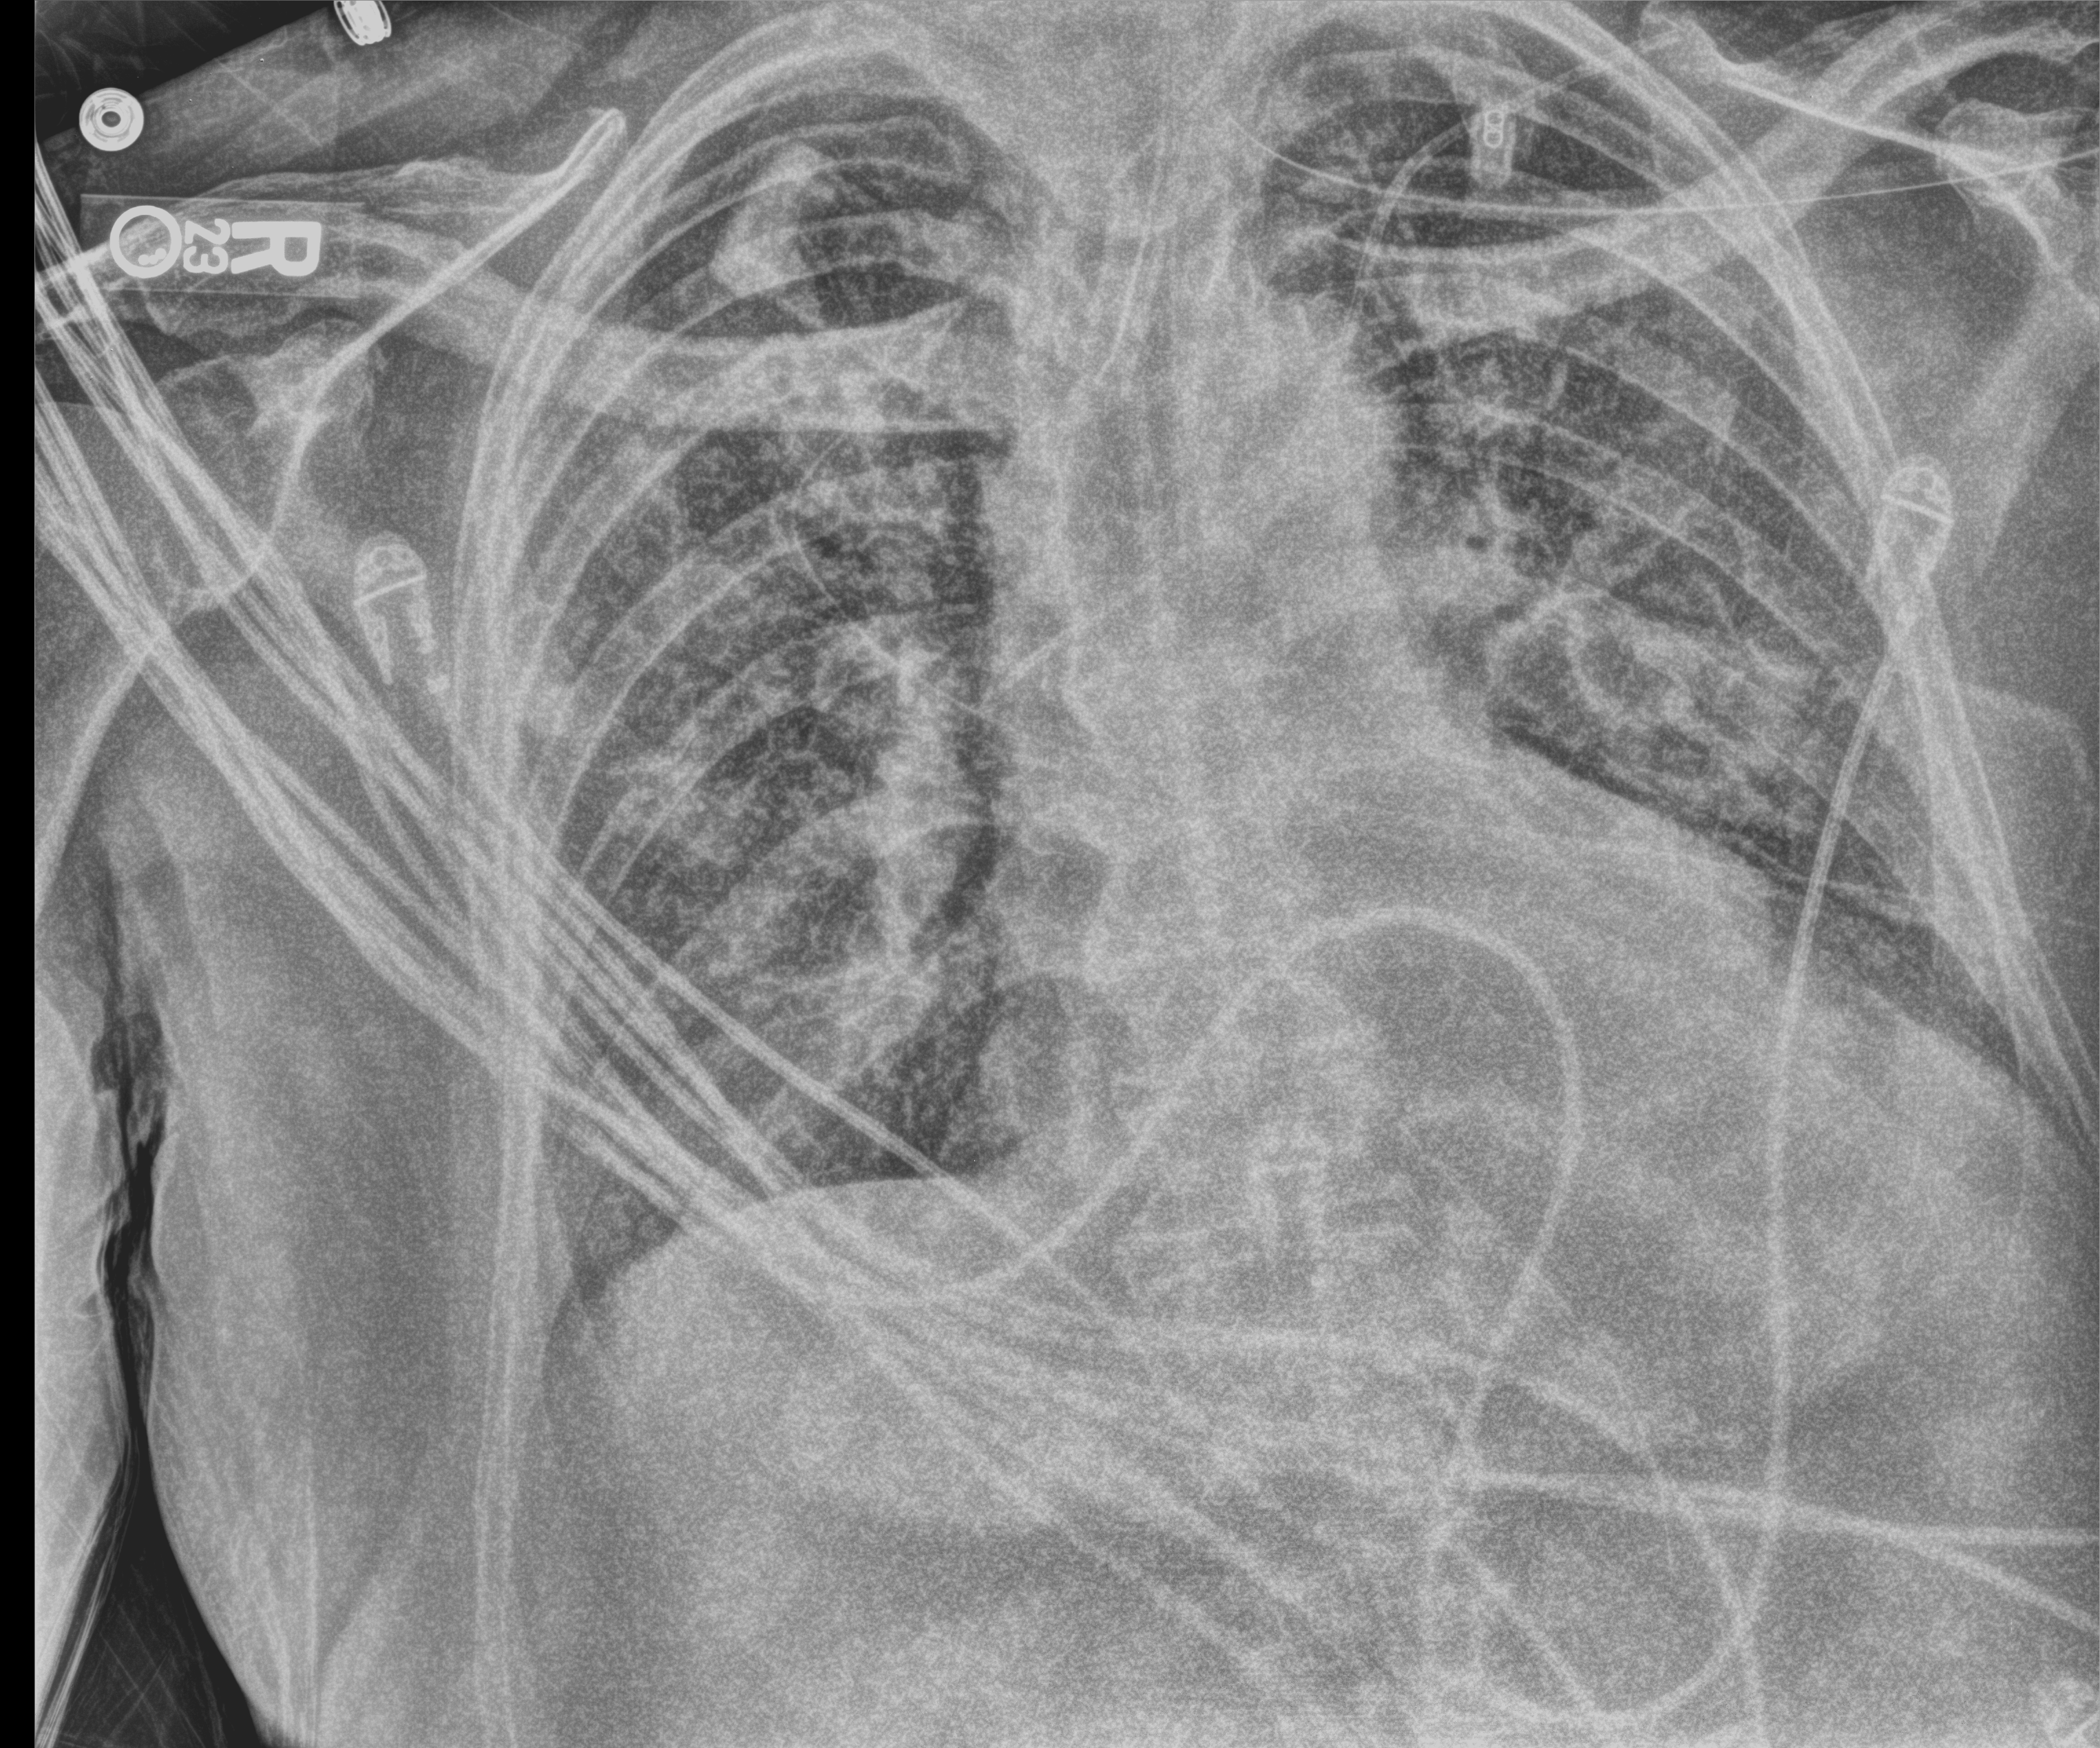
Portable chest radiograph; anteroposterior (AP) projection. Male patient hospitalised with COVID-19, age 75–90 years.
Hospital-stay facts (about this admission, not read from this image; timing relative to this image not recorded):
- mechanically ventilated during this hospital stay: yes
- admitted to intensive care during this hospital stay: yes
- chronic kidney disease (admission record): no